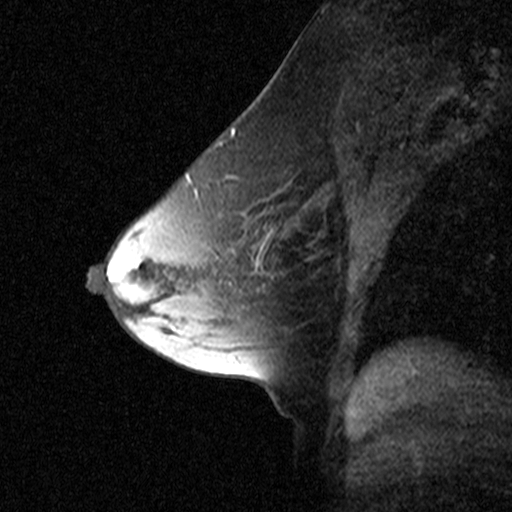
Breast MRI (dynamic contrast-enhanced), one sagittal slice. Position 27 of 44 along the scan axis. Dynamic contrast-enhanced study with each time point stored as its own series, time point 2 of 3 at this slice position (early post-contrast, ordered by acquisition time). 1.5 T. TE 4.5 ms, TR 11 ms. 512 × 512 image matrix, field of view 200 × 200 mm. Female patient, age 53 years. Case-level facts recorded for this patient, not image findings: setting: breast cancer imaged before/during neoadjuvant chemotherapy; receptor status: HR-positive, HER2-negative.
Outlined on this slice (semi-automatically segmented with operator editing):
- analysis volume of interest (the breast-tissue region the enhancement analysis was run in; not a lesion): box from (x=170, y=150) to (x=277, y=273) px
- tumour enhancement mask (voxels above the 90 % enhancement threshold inside the analysis volume of interest): (x=186, y=175)–(x=191, y=183)